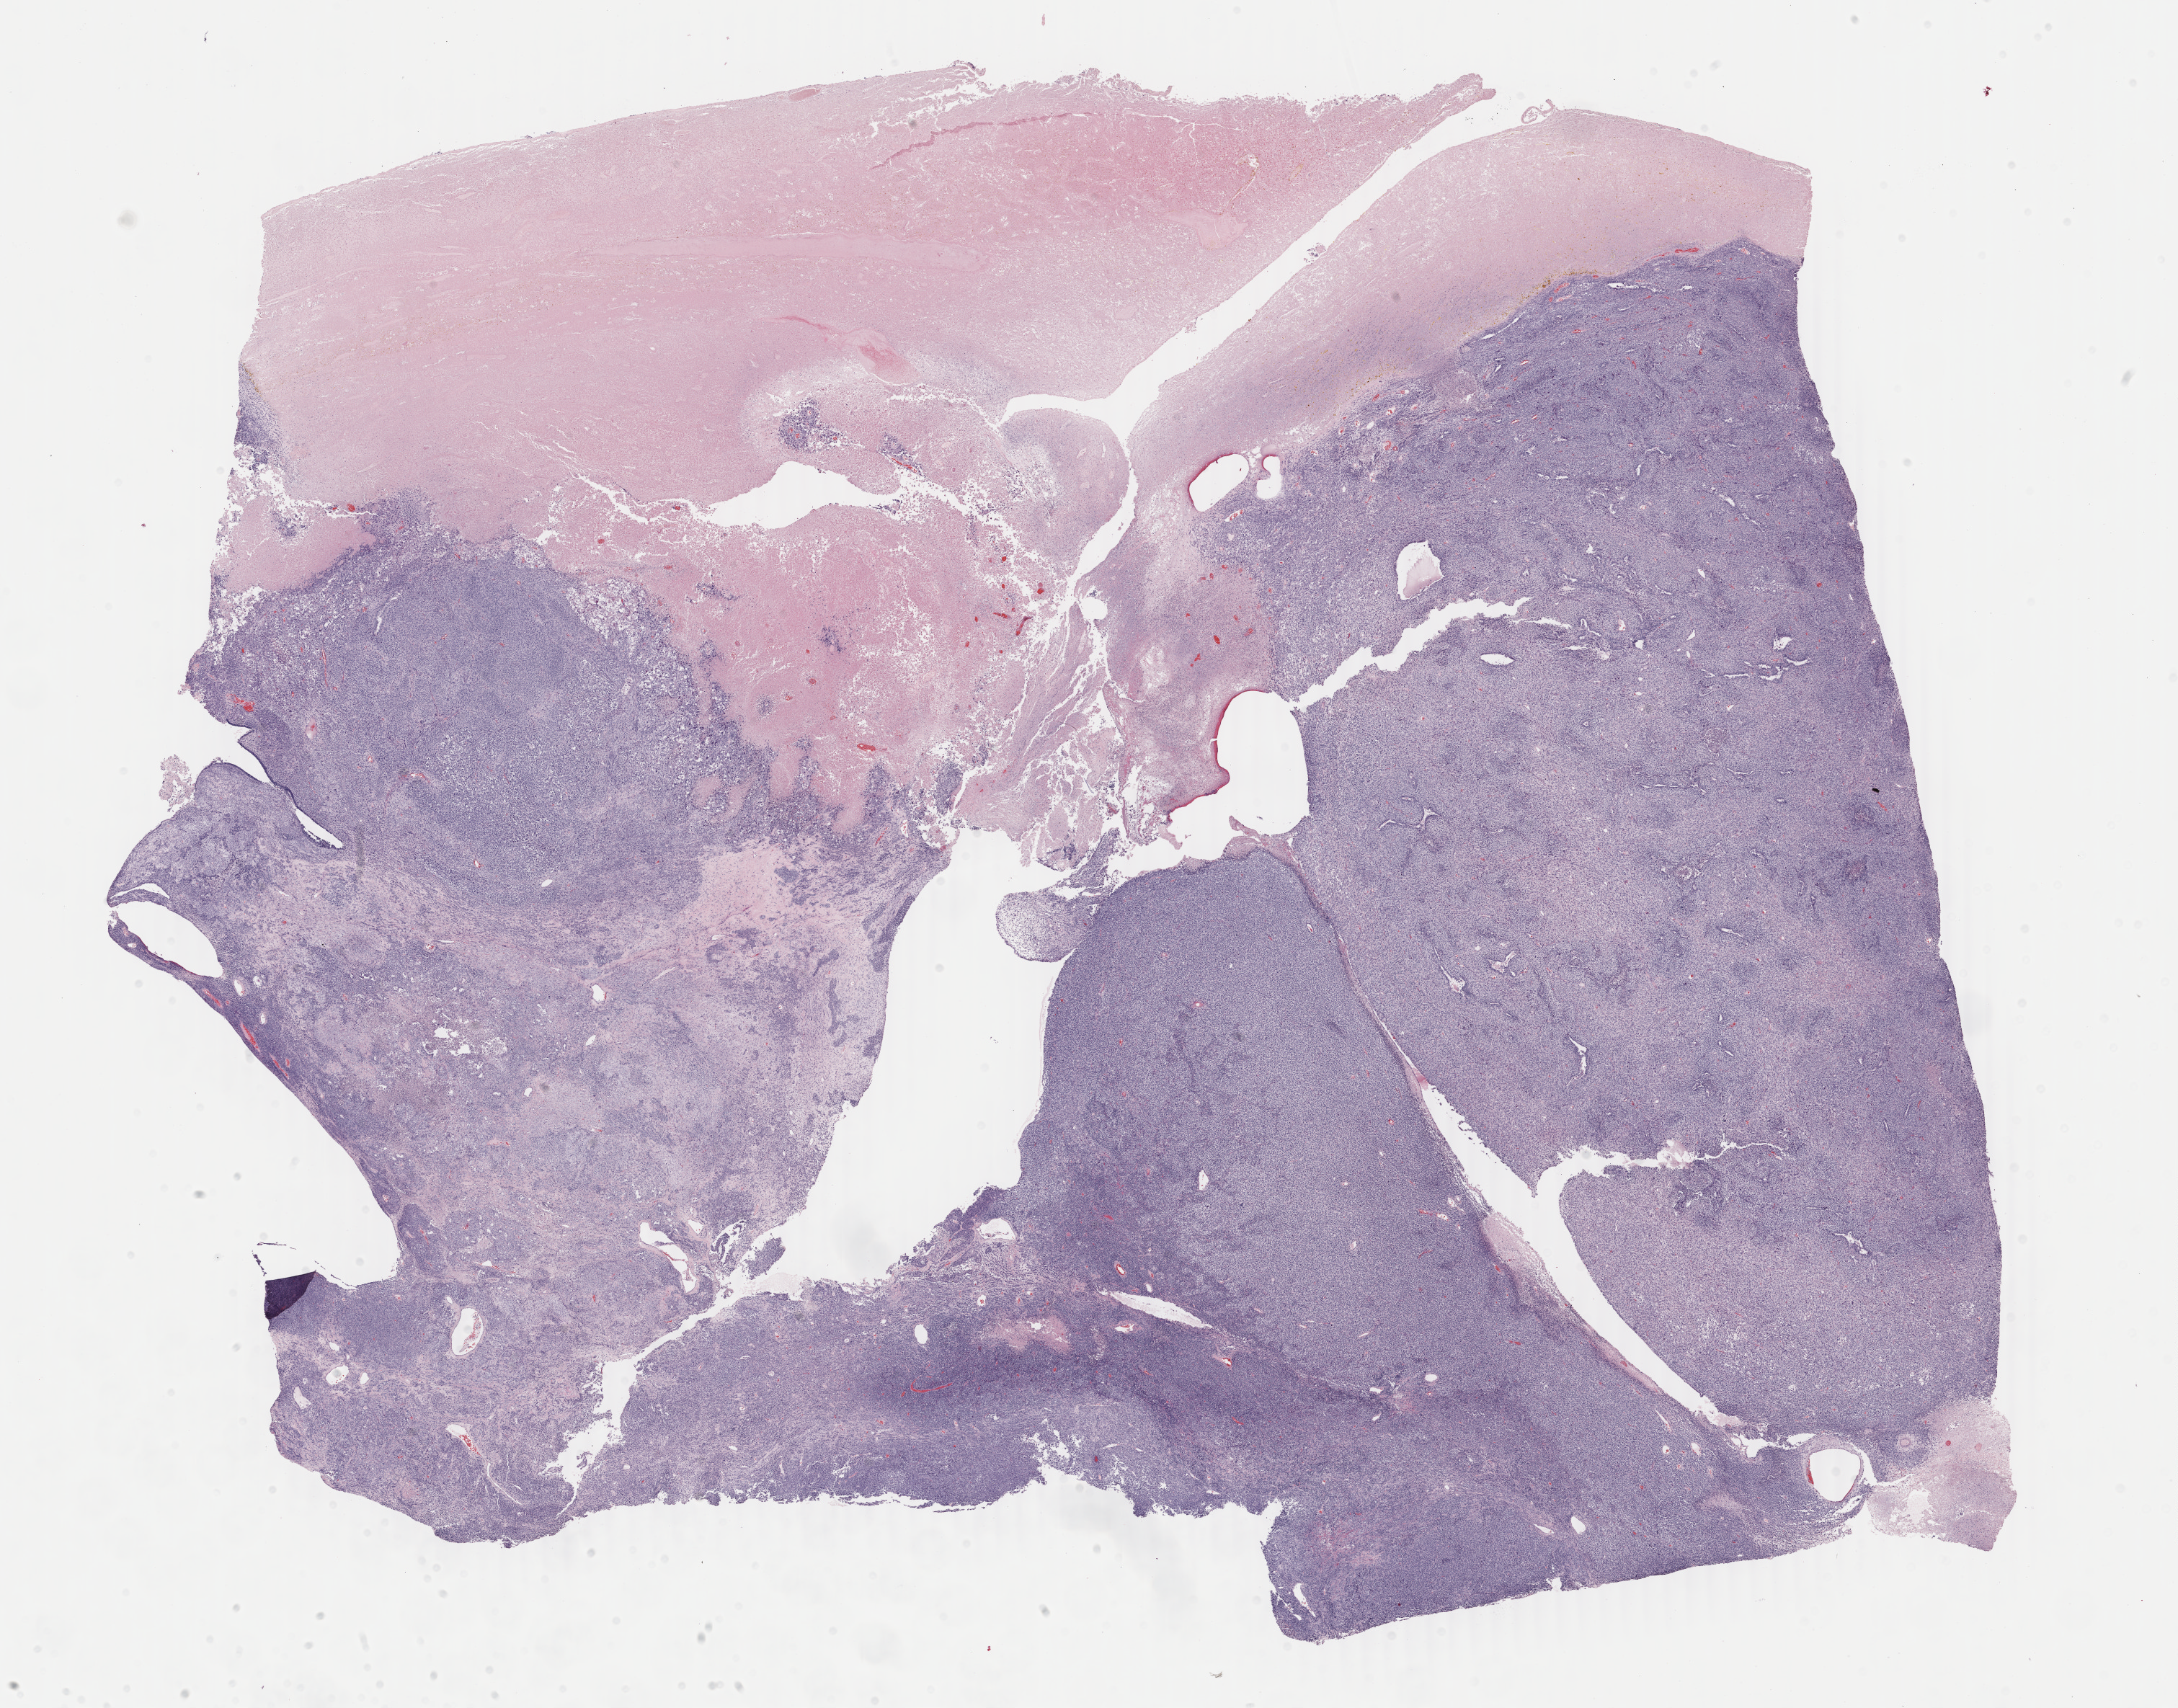
Digitized H&E-stained tissue section (whole slide), whole scanned area (about 24.0 x 18.8 mm, acquisition: 40x scan) shown as a low-resolution overview. Formalin-fixed paraffin-embedded (FFPE) diagnostic section. Primary tumour sample from the uterus. Patient: female, age at initial diagnosis 62 years.
FIGO stage: IVB. Diagnosis: Mullerian mixed tumor (endometrium).